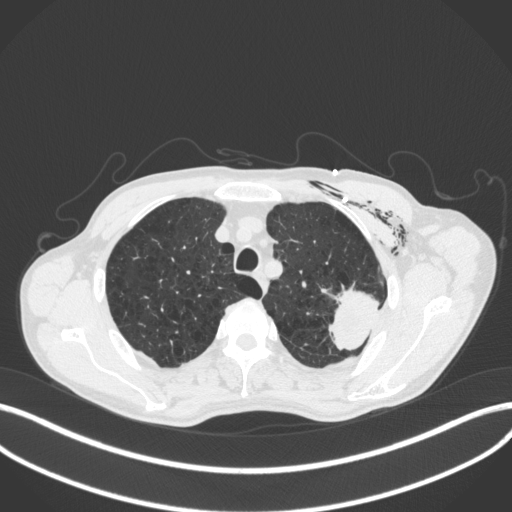
Chest CT, one axial slice; reconstruction kernel B31f; lung window (W 1500 / L -600 HU); 1 mm slice thickness; 512 × 512 image matrix, field of view 400 × 400 mm. Patient: male, 58 years. Case-level facts recorded for this patient, not image findings: clinical TNM (as recorded): T3 N0 M0.
Outlined on this slice (rectangle marked by the reading radiologist):
- lung tumour (recorded histology: adenocarcinoma): bounding box <323,284,384,356> (left, top, right, bottom; pixels)